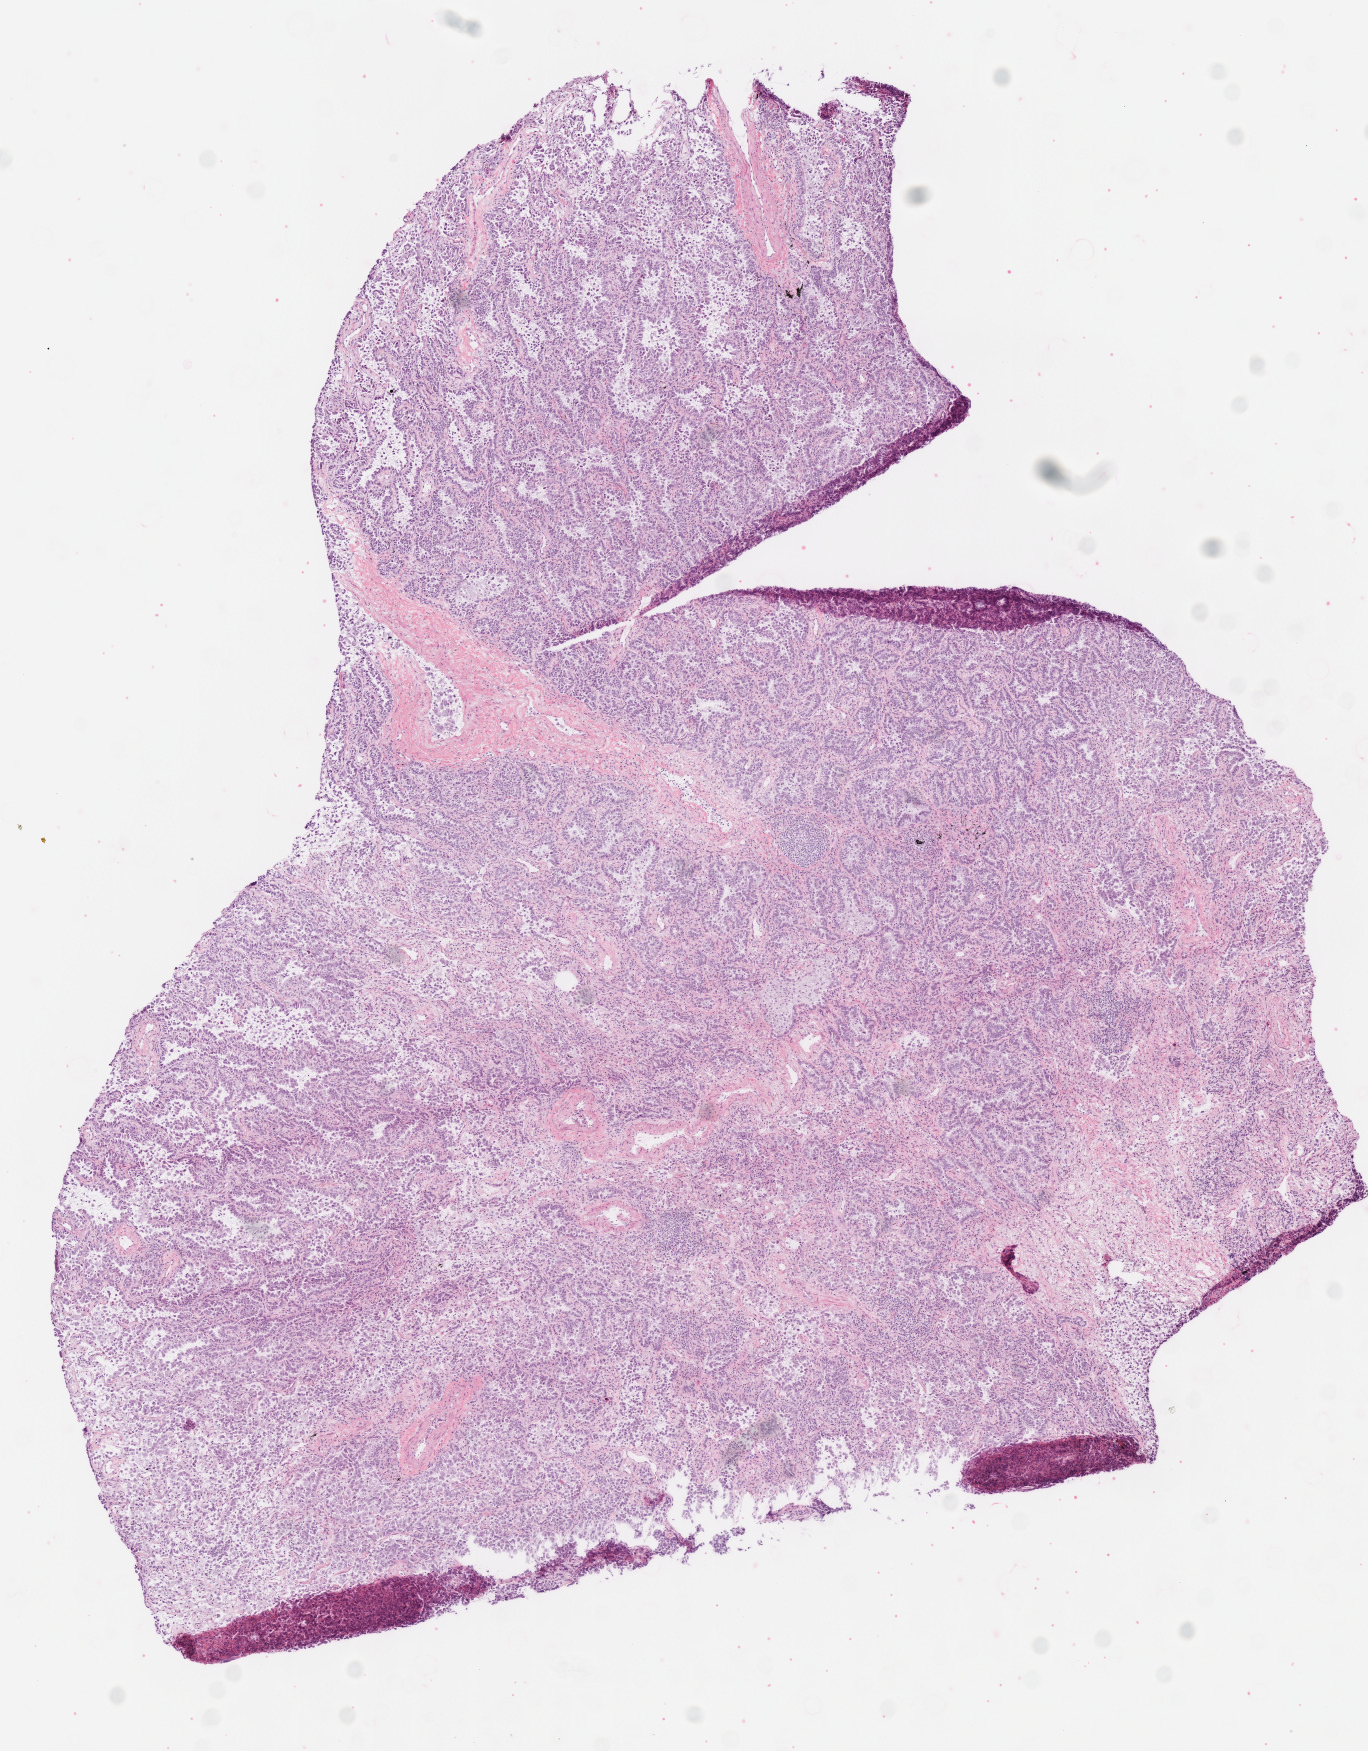
Whole-slide histology image, Hematoxylin and eosin (H&E) stained, whole scanned area (about 5.4 x 6.9 mm) shown as a low-resolution overview, frozen section from the top of the tissue portion, lung, primary tumour sample. Patient: female, age at initial diagnosis 58 years.
Pathologic diagnosis: Bronchiolo-alveolar carcinoma, non-mucinous (lower lobe, lung).